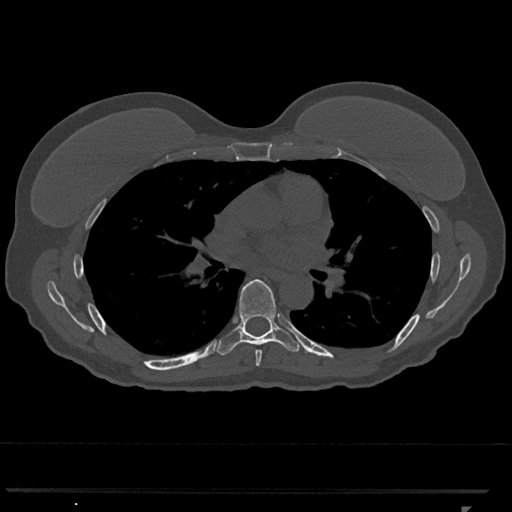
CT including the spine, one axial slice. Reconstruction kernel Br40s/3. 120 kVp. Bone window (W 1800 / L 400 HU). 0.5 mm slice thickness. 512 × 512 image matrix, field of view 380 × 380 mm. Female patient, age 62 years. From the clinical record (not read from this slice): primary cancer: renal.
Structures marked on this image (semi-automatic segmentation, software-assisted and operator-edited):
- T6 vertebra: bounding box (x1, y1, x2, y2) in pixels: (255, 350, 262, 366)
- T7 vertebra: (215, 279, 302, 356)